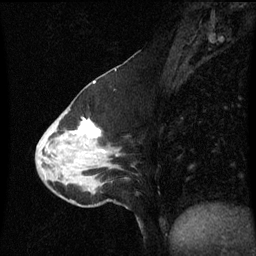
Breast MRI (dynamic contrast-enhanced), one sagittal slice; slice 27 of 60 in the series (ordered by position); dynamic contrast-enhanced series, image 2 of 3 at this slice position (ordered by acquisition); 1.5 T; TE 4.2 ms, TR 8.9 ms; 256 × 256 image matrix, field of view 200 × 200 mm. Patient: female, 50 years. From the clinical record (not read from this slice): setting: breast cancer imaged before/during neoadjuvant chemotherapy; receptor status: HR-positive, HER2-negative.
Annotated regions visible in this slice (semi-automatic segmentation, software-assisted and operator-edited):
- analysis volume of interest (the breast-tissue region the enhancement analysis was run in; not a lesion): bounding box [x1, y1, x2, y2] px = [37, 100, 121, 207]
- tumour enhancement mask (voxels above the 70 % enhancement threshold inside the analysis volume of interest): [73, 120, 101, 139]